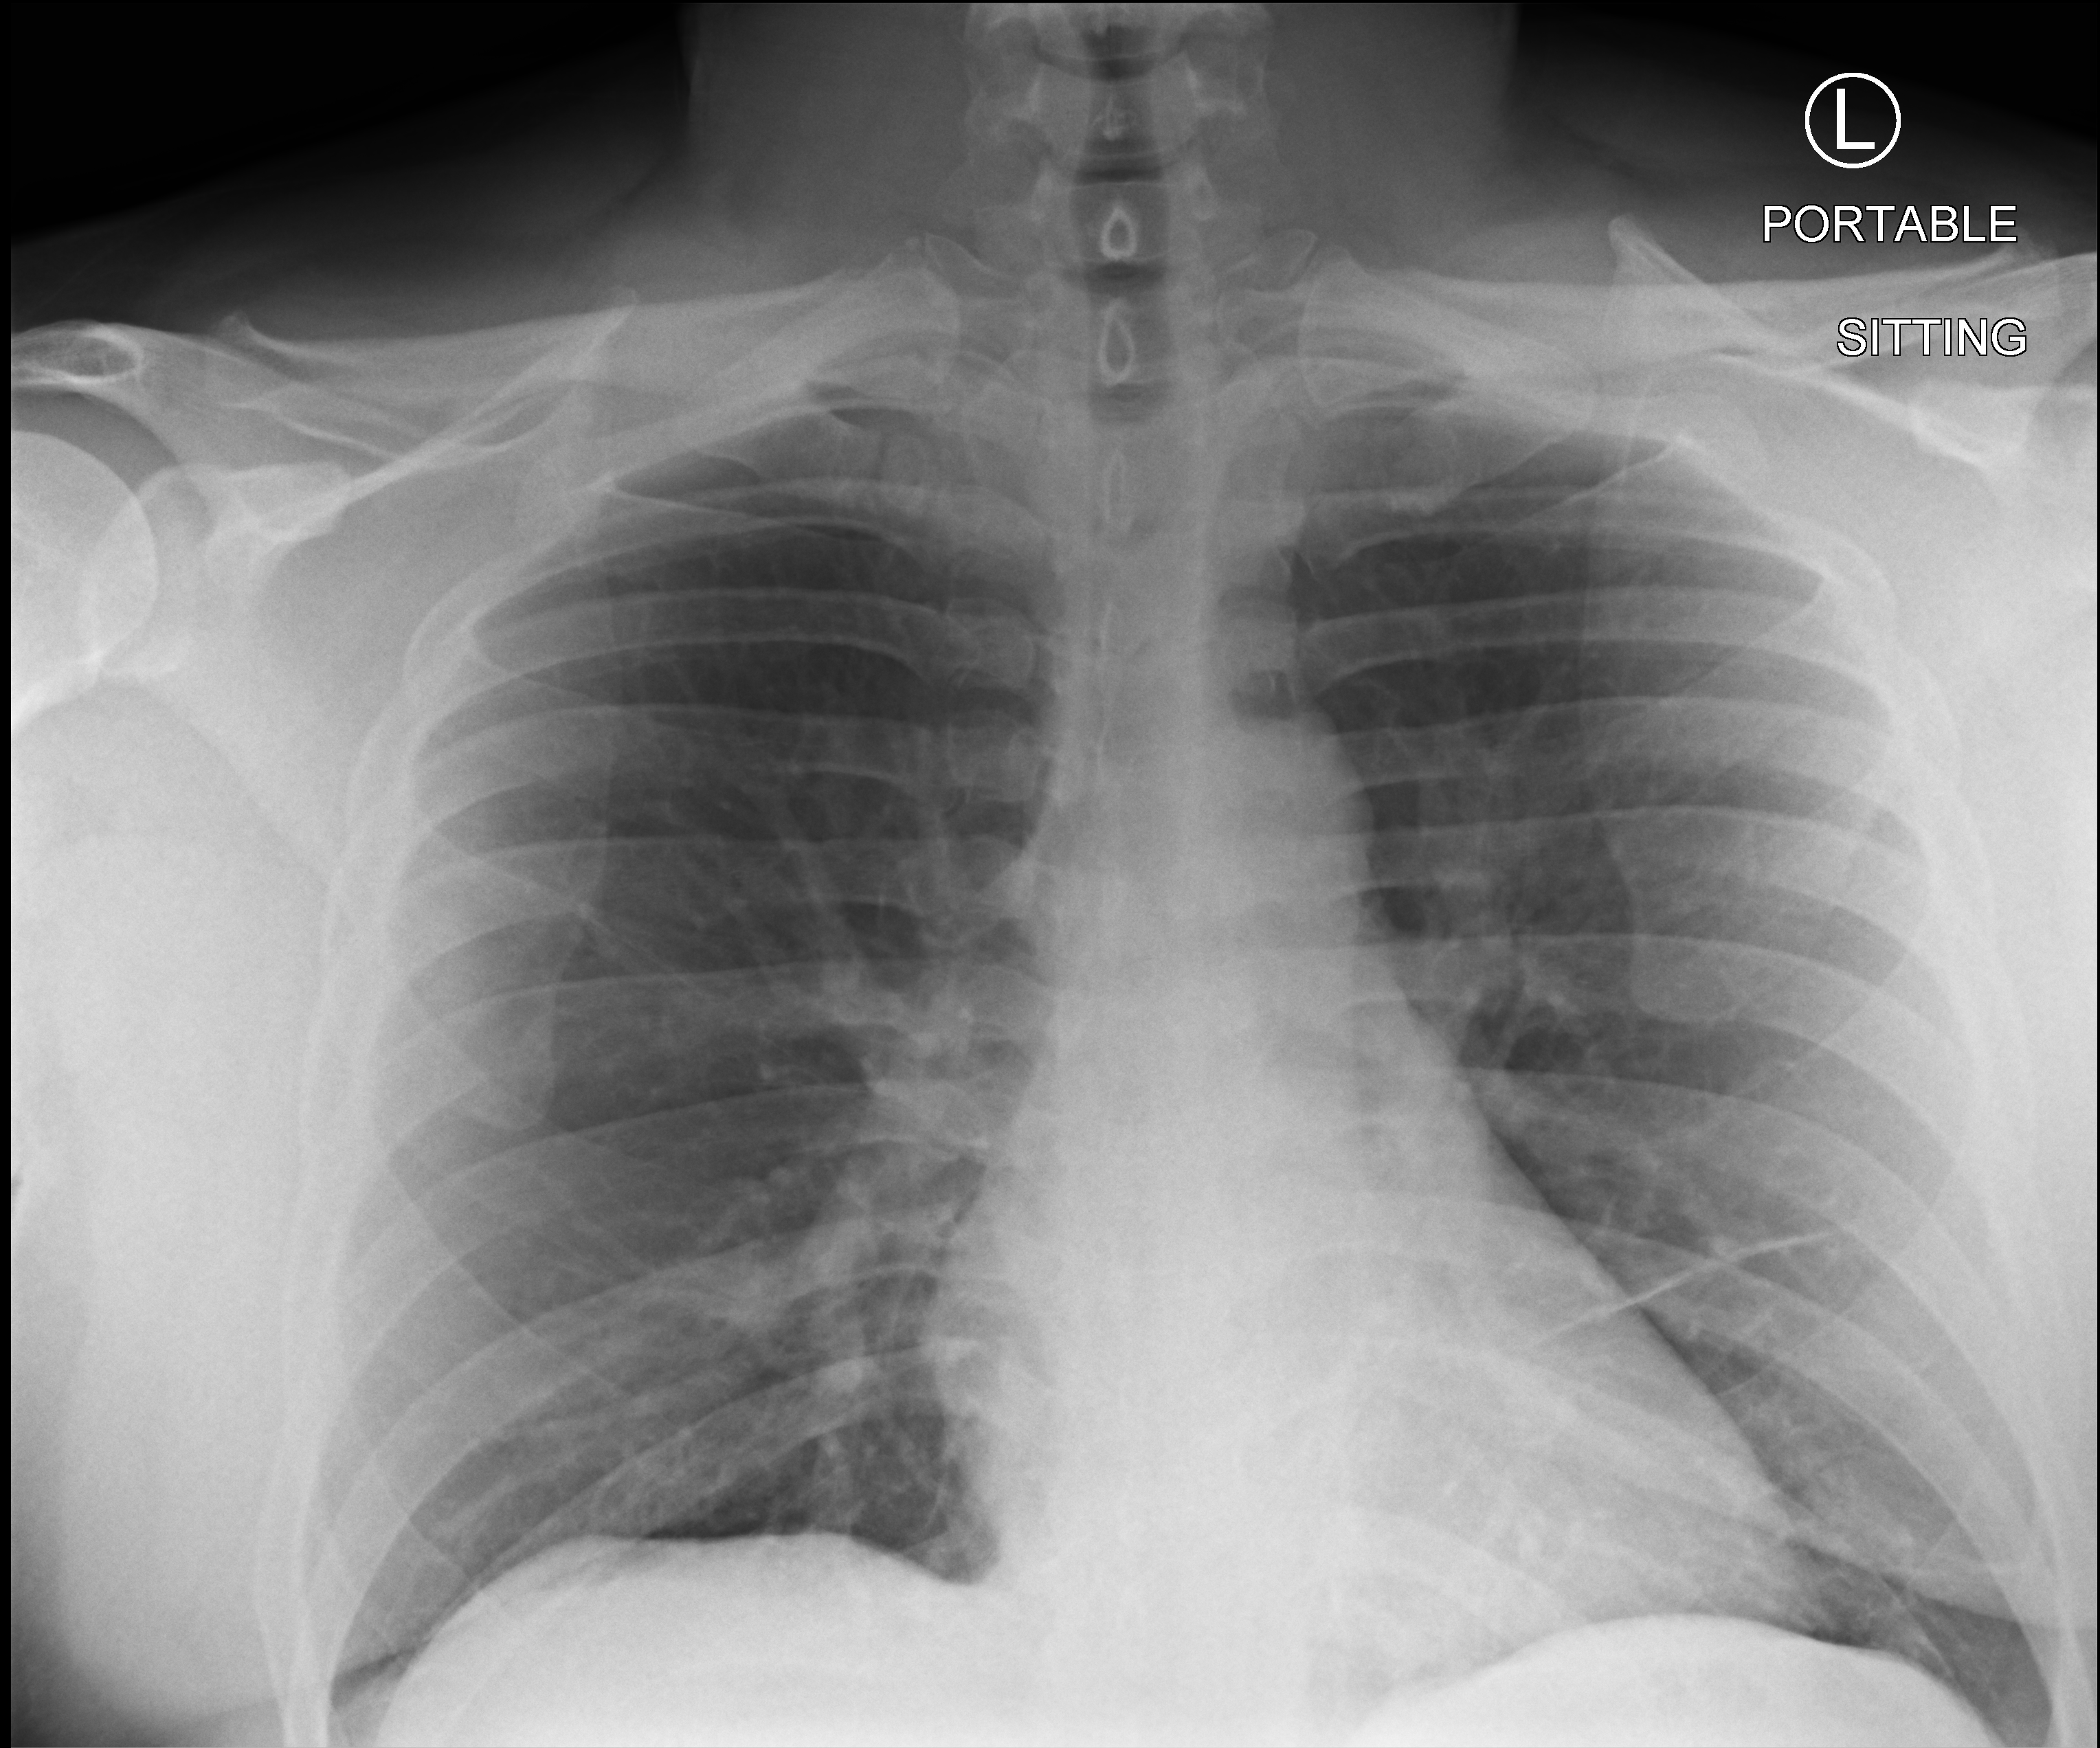
Chest X-ray (portable); anteroposterior (AP) projection. Patient hospitalised with COVID-19; male, aged 18–59 years.
Admission-level facts for this patient (not findings on this image; timing relative to this image not recorded):
- mechanically ventilated during this hospital stay: no